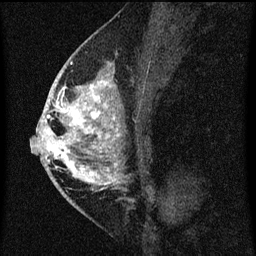
Breast MRI (dynamic contrast-enhanced), one sagittal slice; slice 34 of 60 in the series (ordered by position); dynamic contrast-enhanced series, image 2 of 3 at this slice position (ordered by acquisition); 1.5 T; TE 4.2 ms, TR 8 ms; 256 × 256 image matrix, field of view 180 × 180 mm. Female patient, age 46 years.
Outlined on this slice (semi-automatic segmentation, software-assisted and operator-edited):
- analysis volume of interest (the breast-tissue region the enhancement analysis was run in; not a lesion): box from (x=48, y=68) to (x=122, y=195) px
- tumour enhancement mask (voxels above the 70 % enhancement threshold inside the analysis volume of interest): (x=48, y=70)–(x=120, y=191)